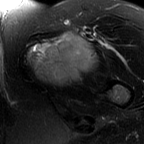
MRI of an extremity soft-tissue mass, one axial slice. T2-weighted fat-saturated. MR volume resampled by the dataset authors to the PET/CT grid (not the native acquisition matrix). 3.27 mm slice thickness. 144 × 144 image matrix. Female patient. Case-level facts recorded for this patient, not image findings: histological type: pleiomorphic leiomyosarcoma; grade: intermediate; site of the primary tumour: left thigh.
Annotated regions visible in this slice (expert contour drawn on MRI and transferred to this co-registered scan by the dataset authors):
- gross tumour volume including surrounding oedema: bounding box <25,32,94,86> (left, top, right, bottom; pixels)
- gross tumour volume (mass): <29,33,94,86>